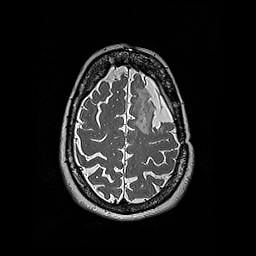
Brain MRI from a brain-tumour surgery series, one axial slice. Position 142 of 192 along the scan axis. 1 mm slice thickness. 256 × 256 image matrix, field of view 250 × 250 mm. Case-level facts recorded for this patient, not image findings: histopathology: Oligodendroglioma; WHO grade: 2.
Structures marked on this image (outlined manually by an expert reader):
- tumour: bounding box (x1, y1, x2, y2) in pixels: (145, 112, 153, 133)